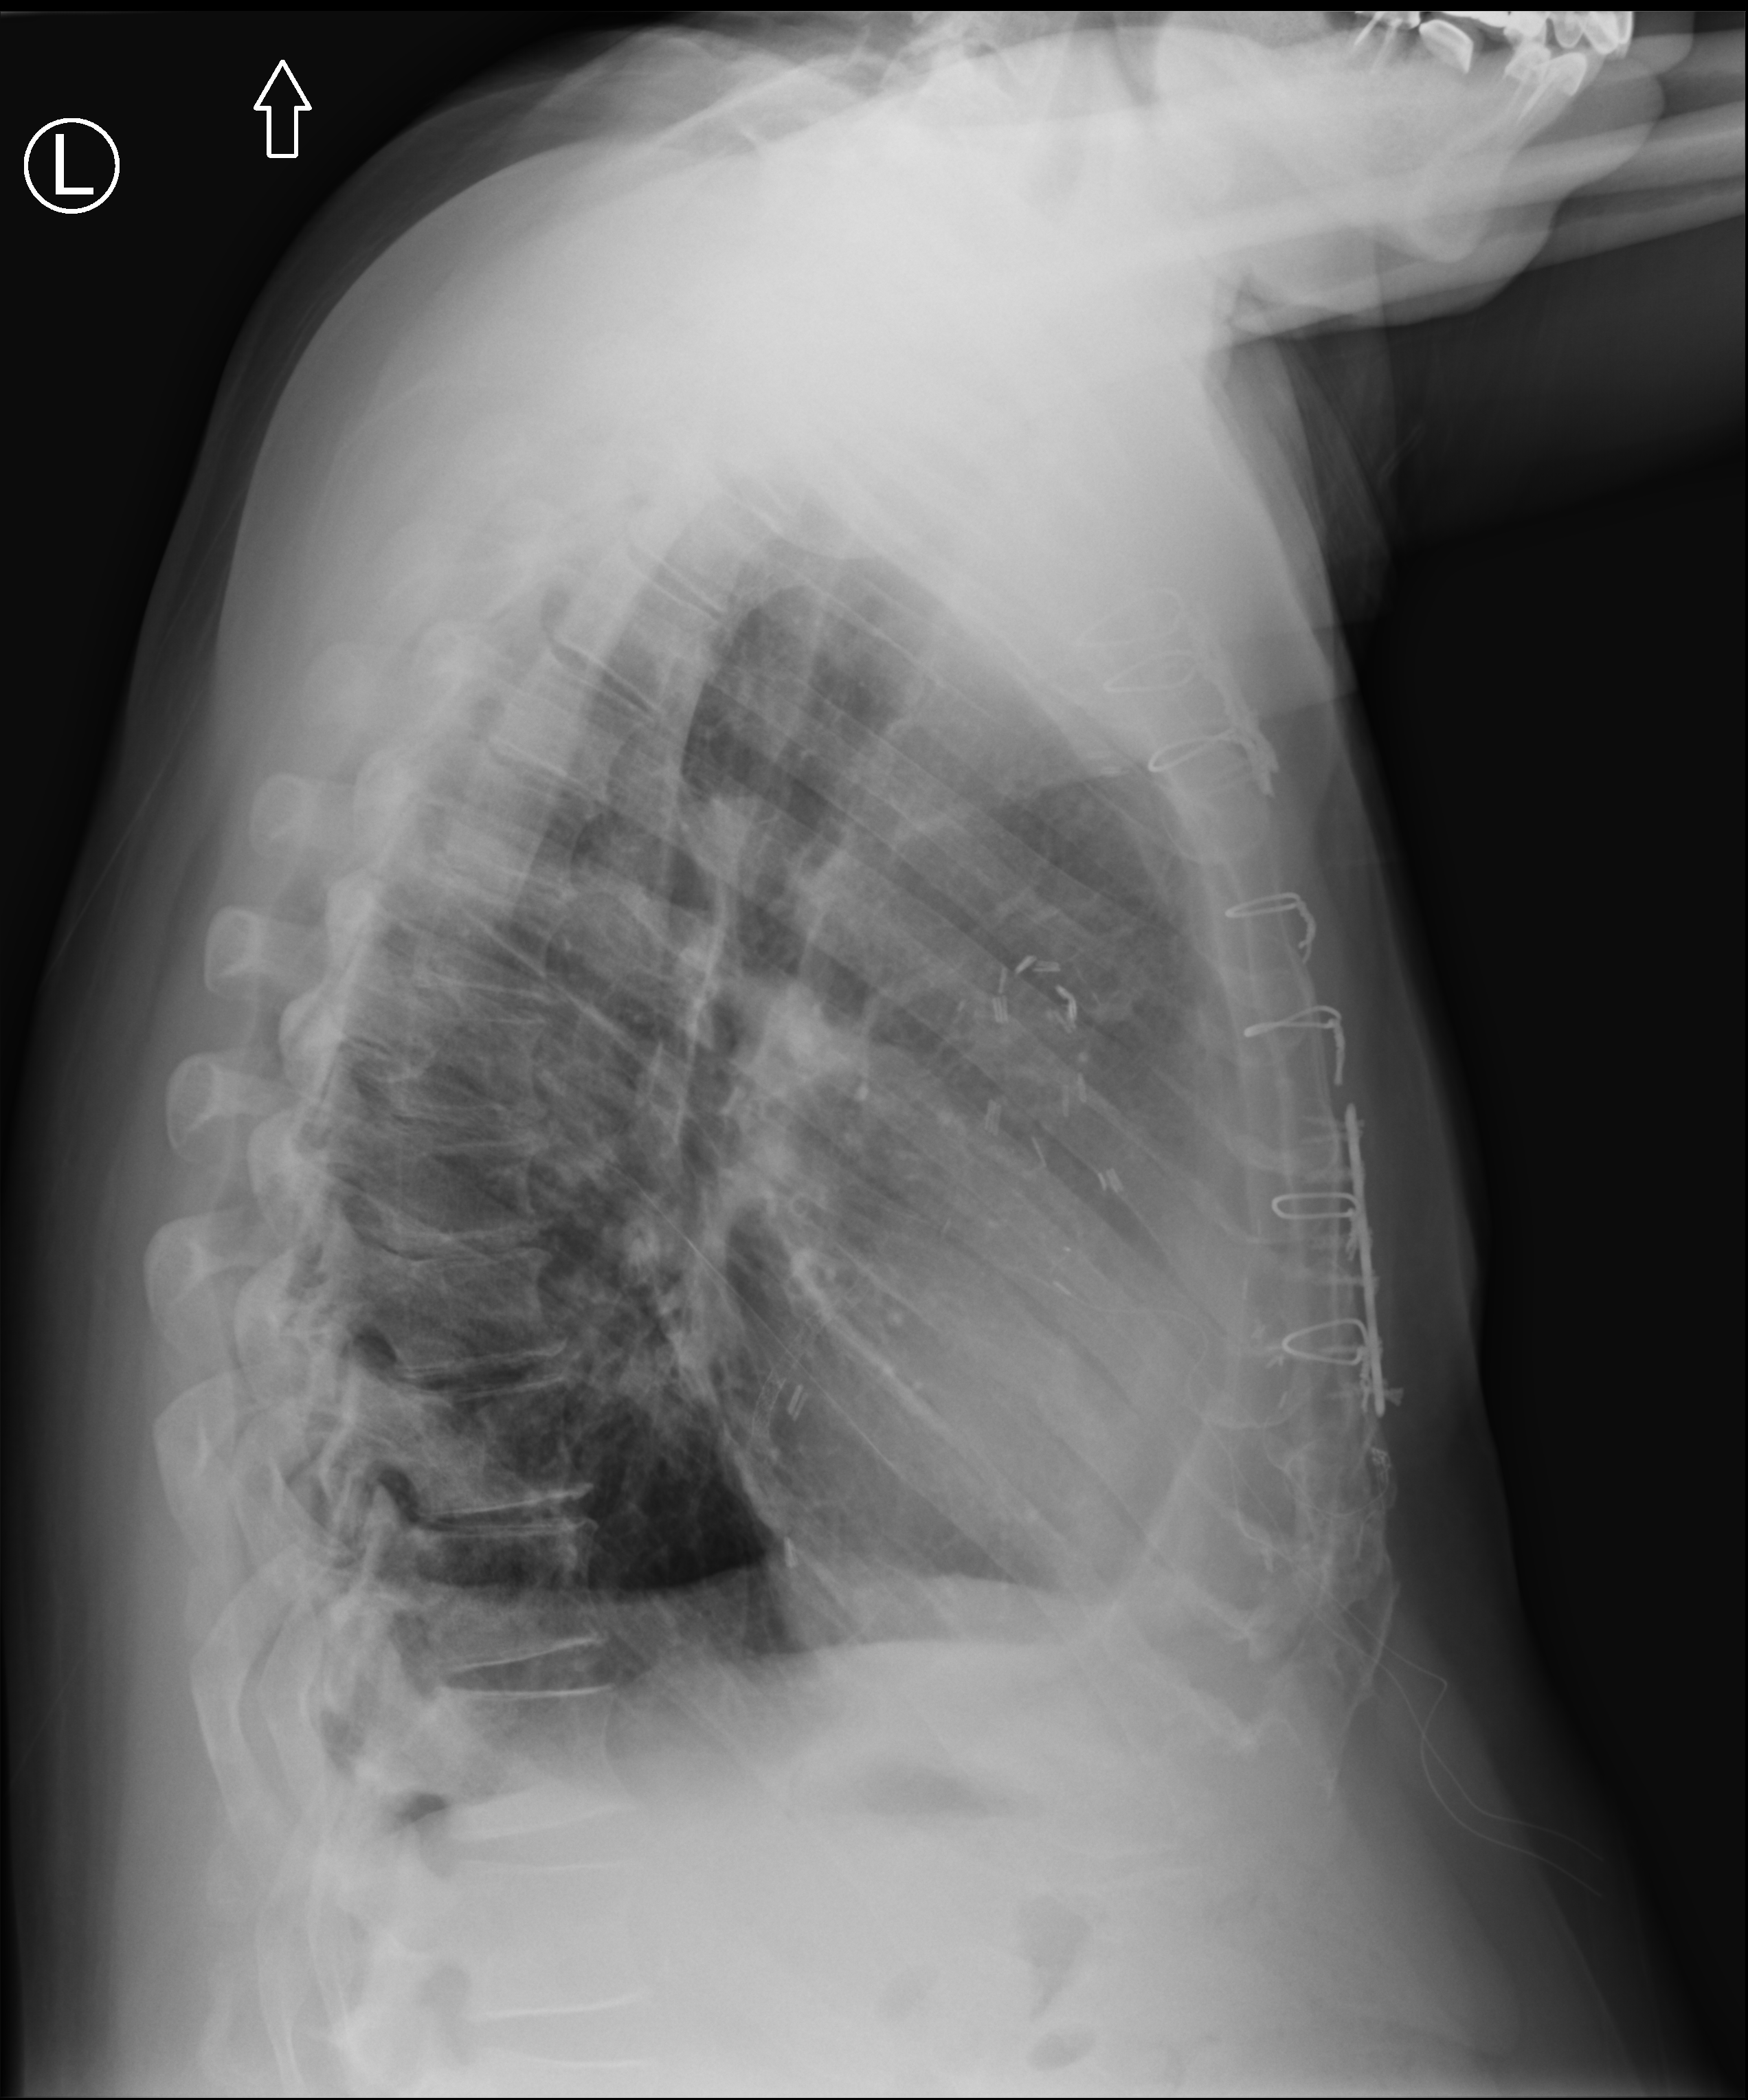
Chest radiograph (computed radiography), lateral projection. Male patient hospitalised with COVID-19, age 60–74 years.
Hospital-stay facts (about this admission, not read from this image; timing relative to this image not recorded): admitted to intensive care during this hospital stay: no.